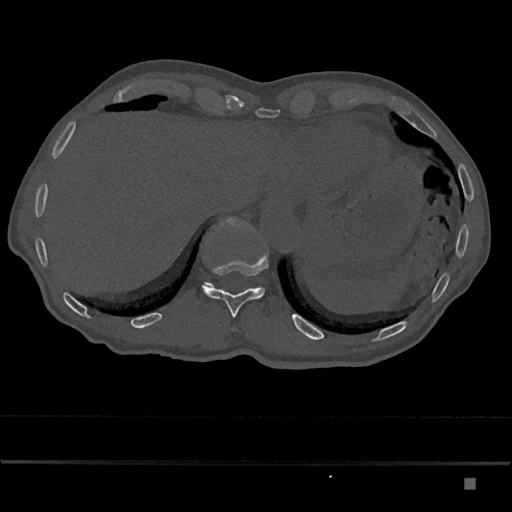
CT including the spine, one axial slice. Slice 667 of 797 in the series (ordered by position). Reconstruction kernel Br40s/3. 120 kVp. Bone window (W 1800 / L 400 HU). 0.5 mm slice thickness. 512 × 512 image matrix. Patient: male, 72 years. Case-level facts recorded for this patient, not image findings: primary cancer: prostate.
Outlined on this slice (semi-automatic segmentation, software-assisted and operator-edited):
- T11 vertebra: bounding box <202,253,268,318> (left, top, right, bottom; pixels)
- T12 vertebra: <204,217,250,287>